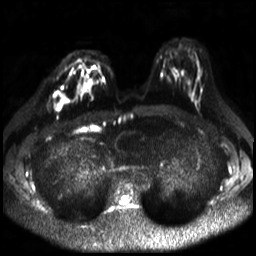
Breast MRI, one axial slice; slice 14 of 30 in the series (ordered by position); diffusion-weighted series; image 2 of 4 stored at this slice position (different b-values; order by instance number); 3 T; 4 mm slice thickness; 256 × 256 image matrix, field of view 320 × 320 mm. Female patient.
Annotated regions visible in this slice (expert manual segmentation):
- tumour on diffusion-weighted imaging: bounding box <52,93,68,110> (left, top, right, bottom; pixels)